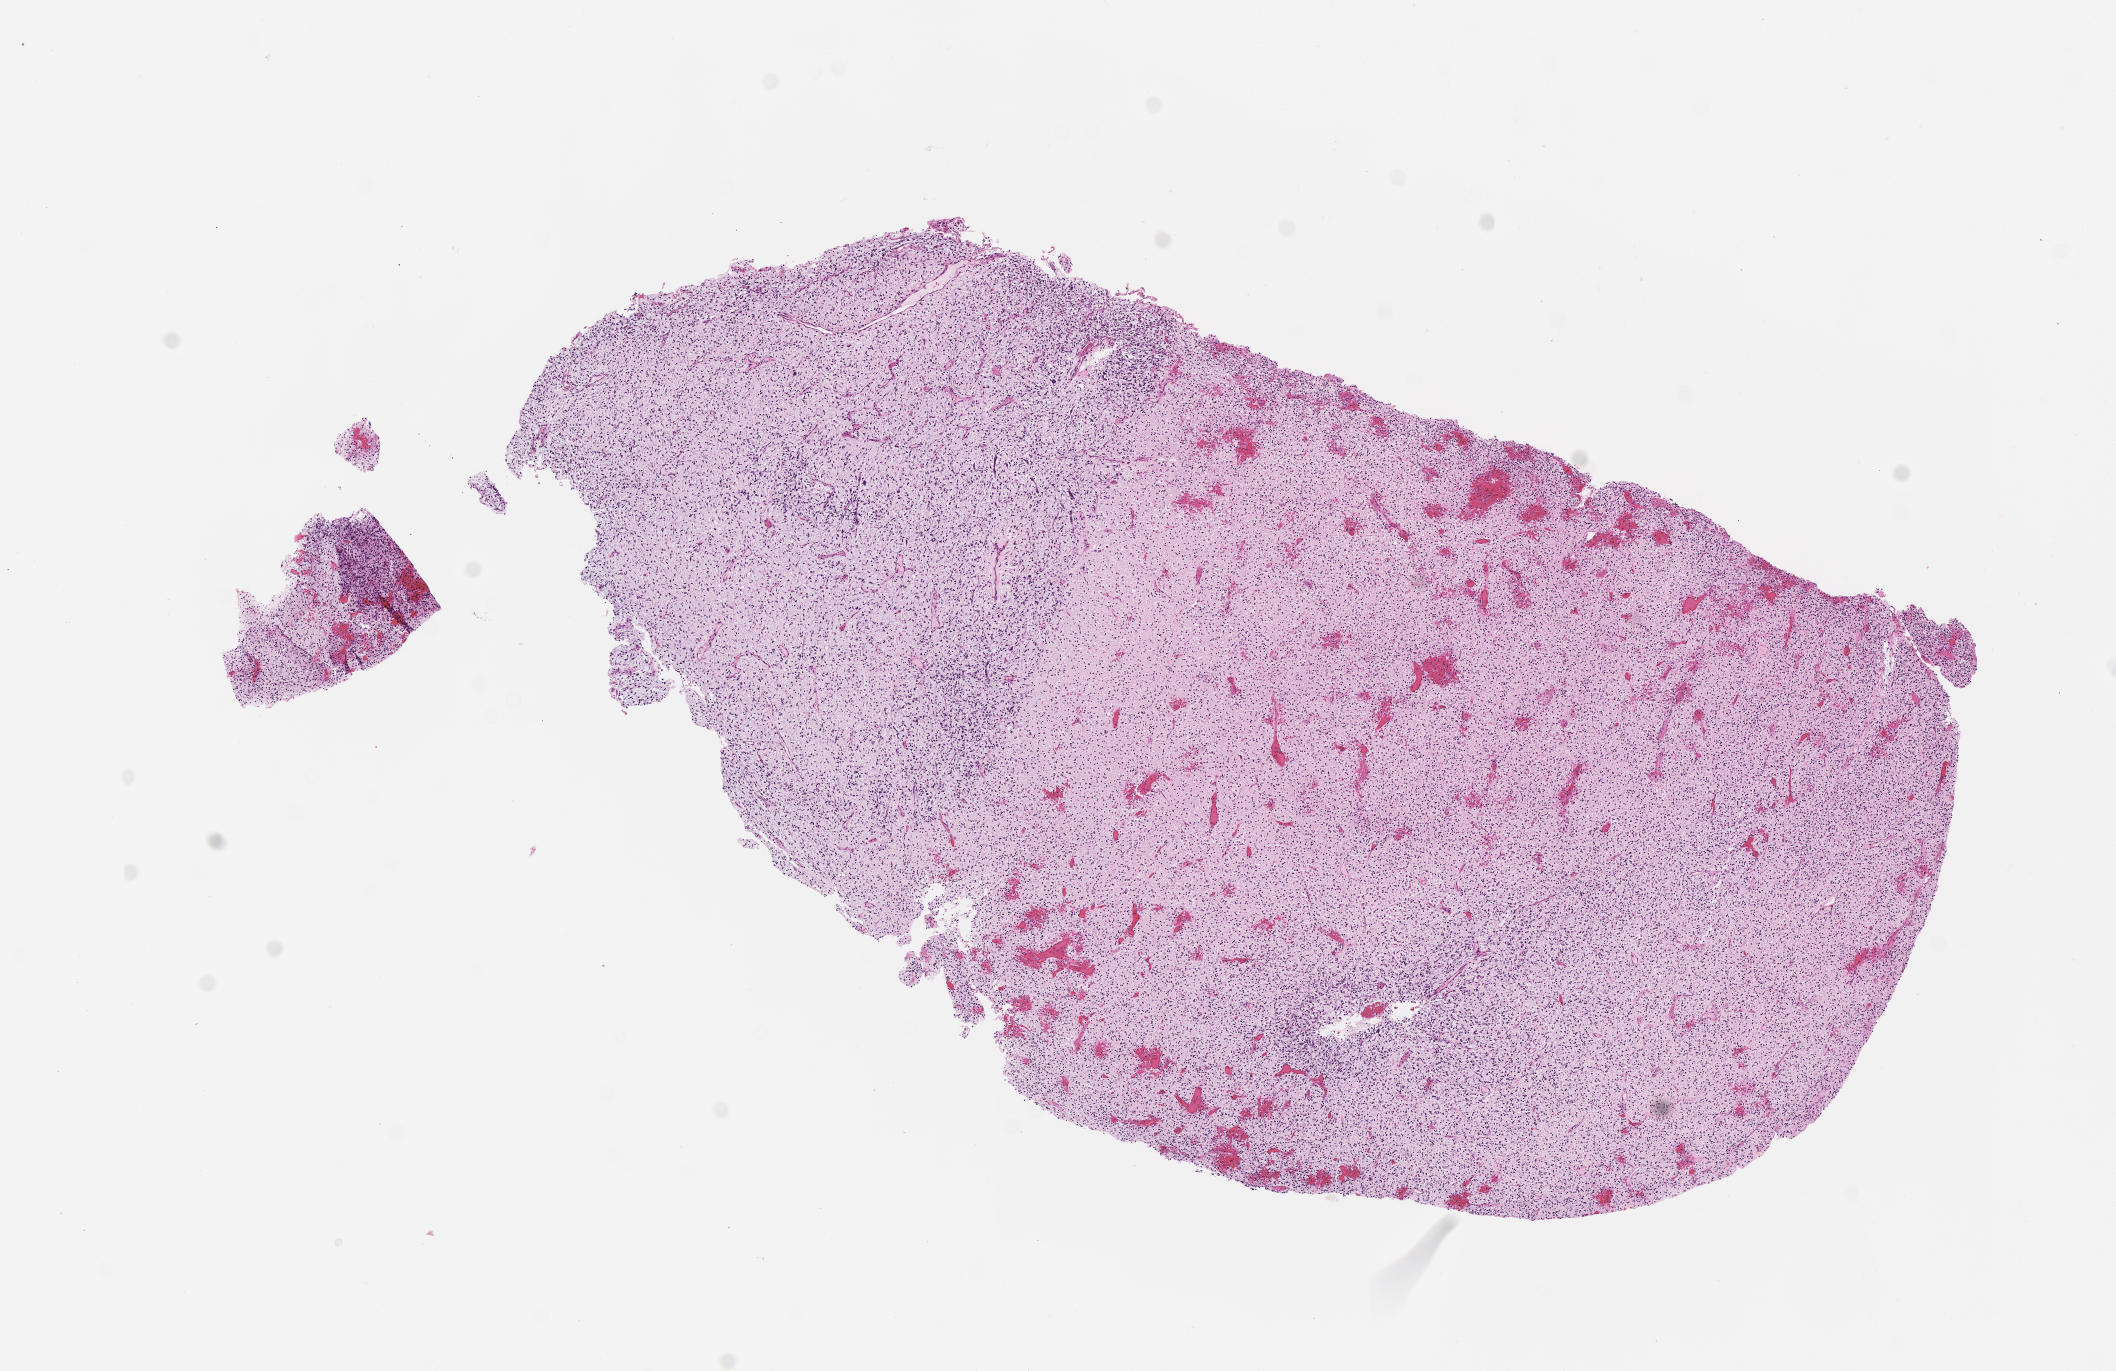
Whole-slide image, hematoxylin and eosin (H&E) stain of tumor tissue — low-resolution overview of the scanned area, about 8.6 x 5.5 mm, formalin-fixed, paraffin-embedded (FFPE) tissue, site: pelvis. Patient: female, age 7.6 years at diagnosis.
- diagnosis: rhabdomyosarcoma; histological classification: embryonal rhabdomyosarcoma
- metastatic status at presentation (as recorded): metastatic
- stage (as recorded): 4